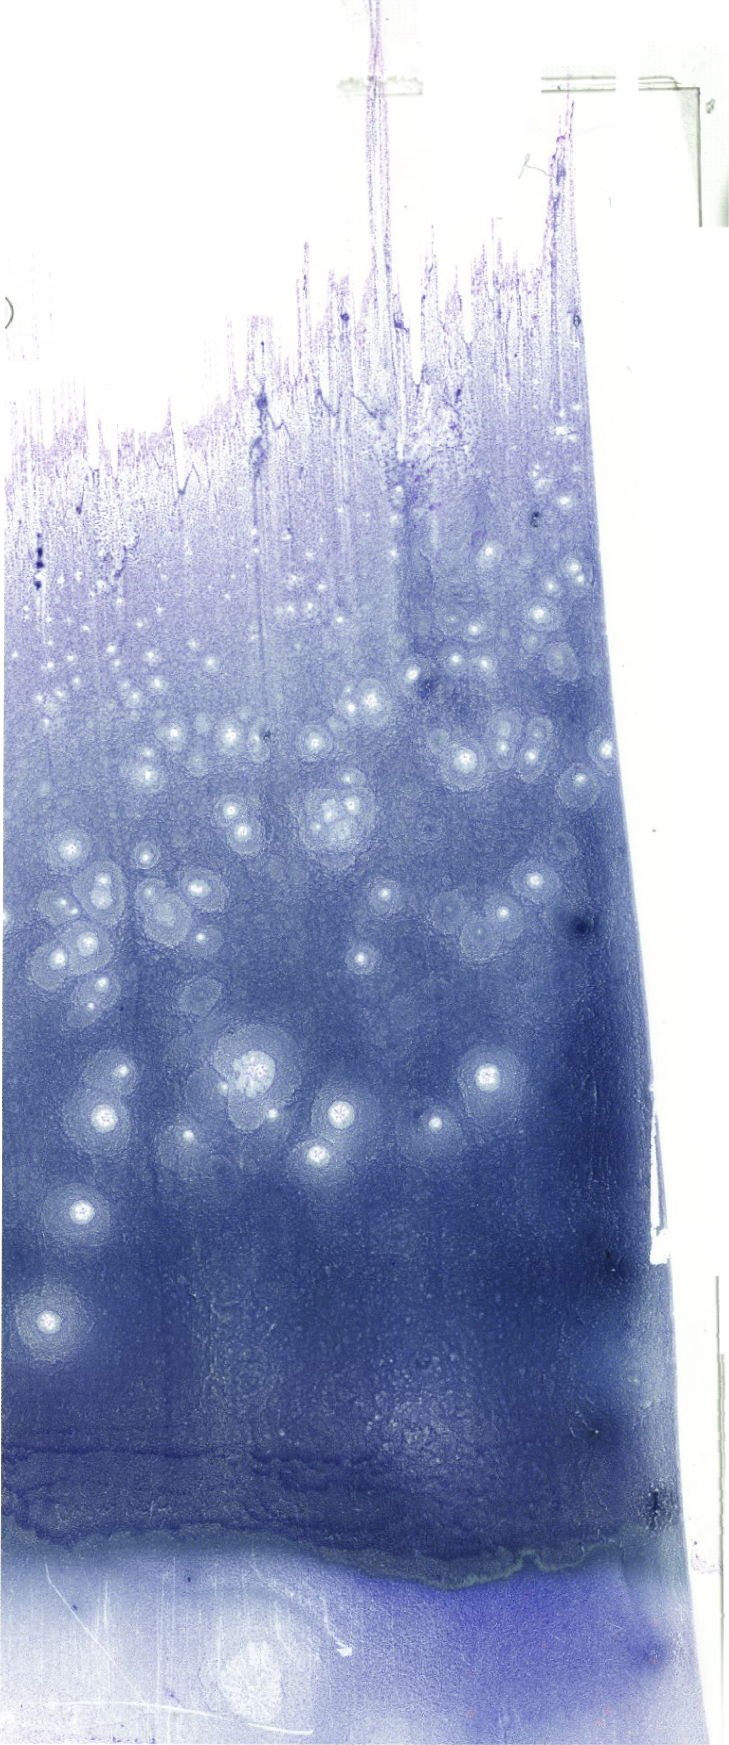
Whole-slide image of a May-Grünwald–Giemsa-stained bone marrow aspirate smear, whole scanned area (about 20.7 x 49.5 mm) shown as a low-resolution overview. Female patient.
Diagnosis: T Acute Lymphoblastic Leukemia.